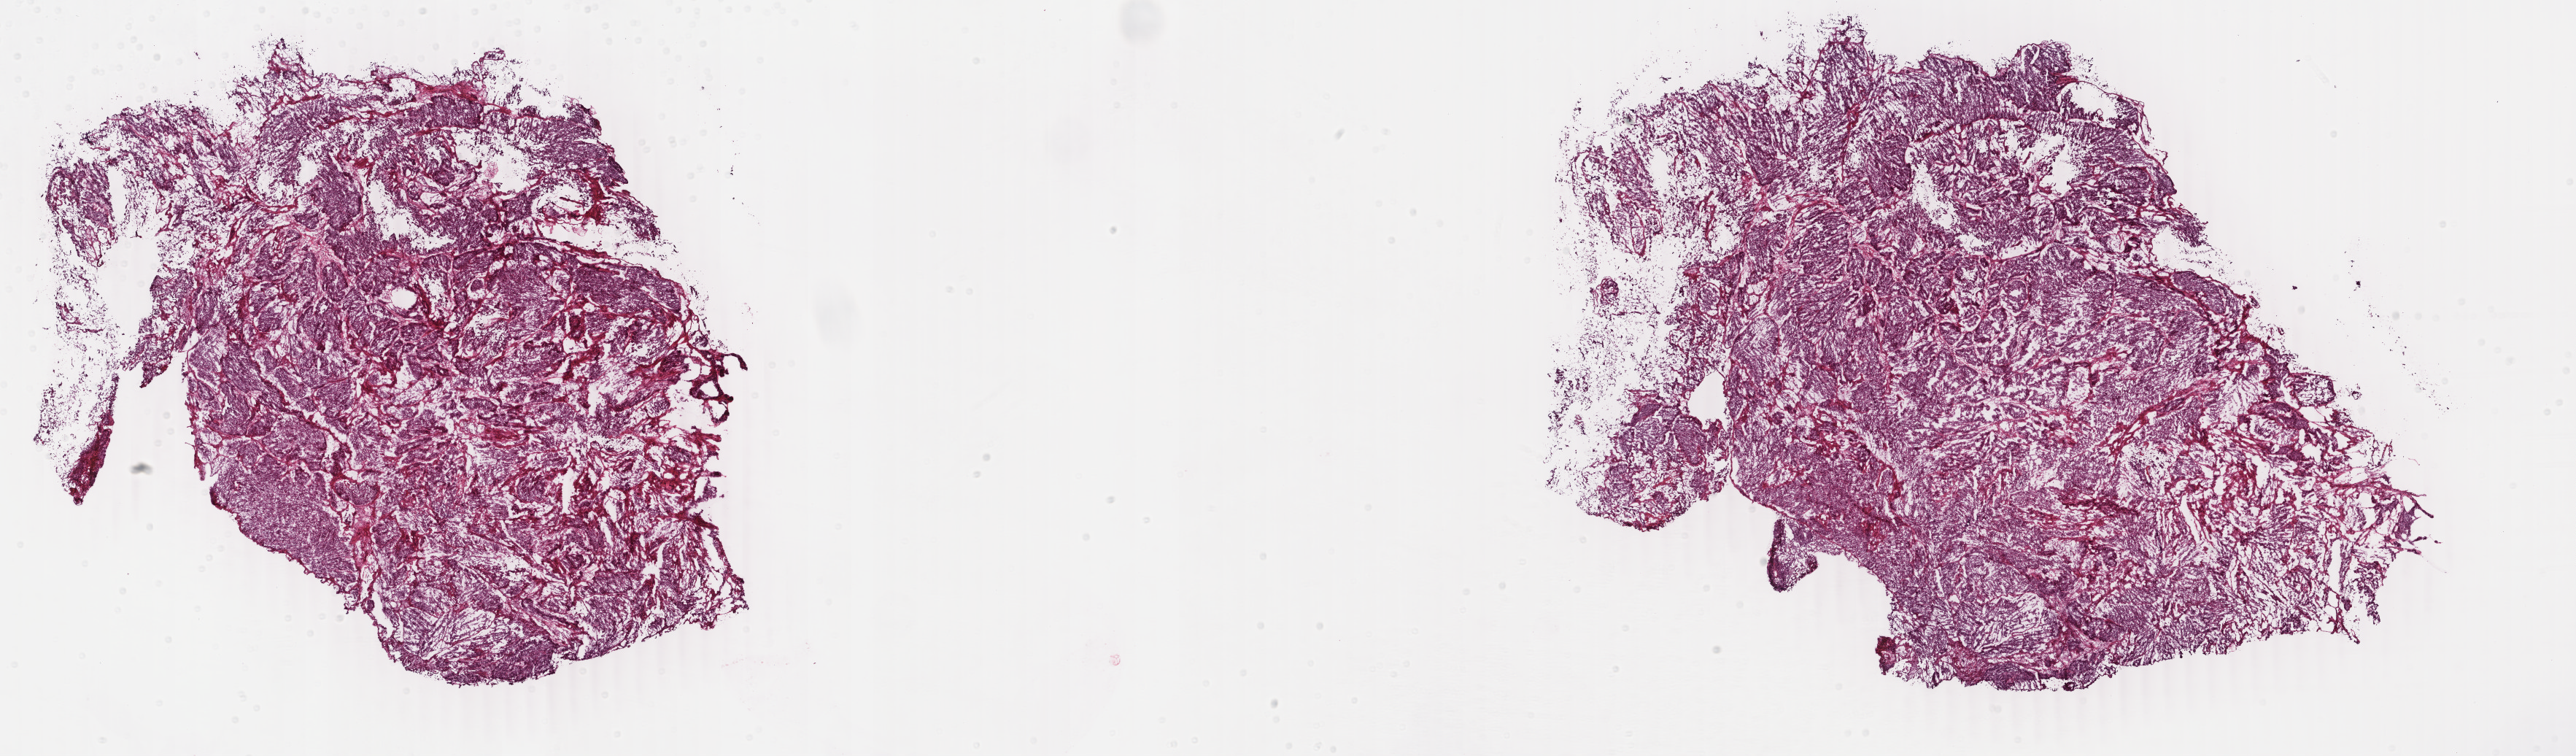
Digitized H&E tissue section (whole slide) — shown as a low-resolution overview of the whole scanned area (about 28.1 x 8.2 mm, acquisition: 40x scan), frozen section, sample: primary tumour, uterus. Female patient; age at initial diagnosis 56 years. Histologic grade: G1 (well differentiated). Slide review estimates, as recorded: tumour cells 80%, tumour nuclei 85%, normal cells 12%, stromal cells 3%, necrosis 5%. Inflammatory infiltration, as recorded: lymphocyte infiltration 0%, monocyte infiltration 0%, neutrophil infiltration 0%.
Lymph nodes positive (case pathology): 0 of 12 examined. Pathologic diagnosis: Endometrioid adenocarcinoma, NOS (endometrium). FIGO stage: IB.